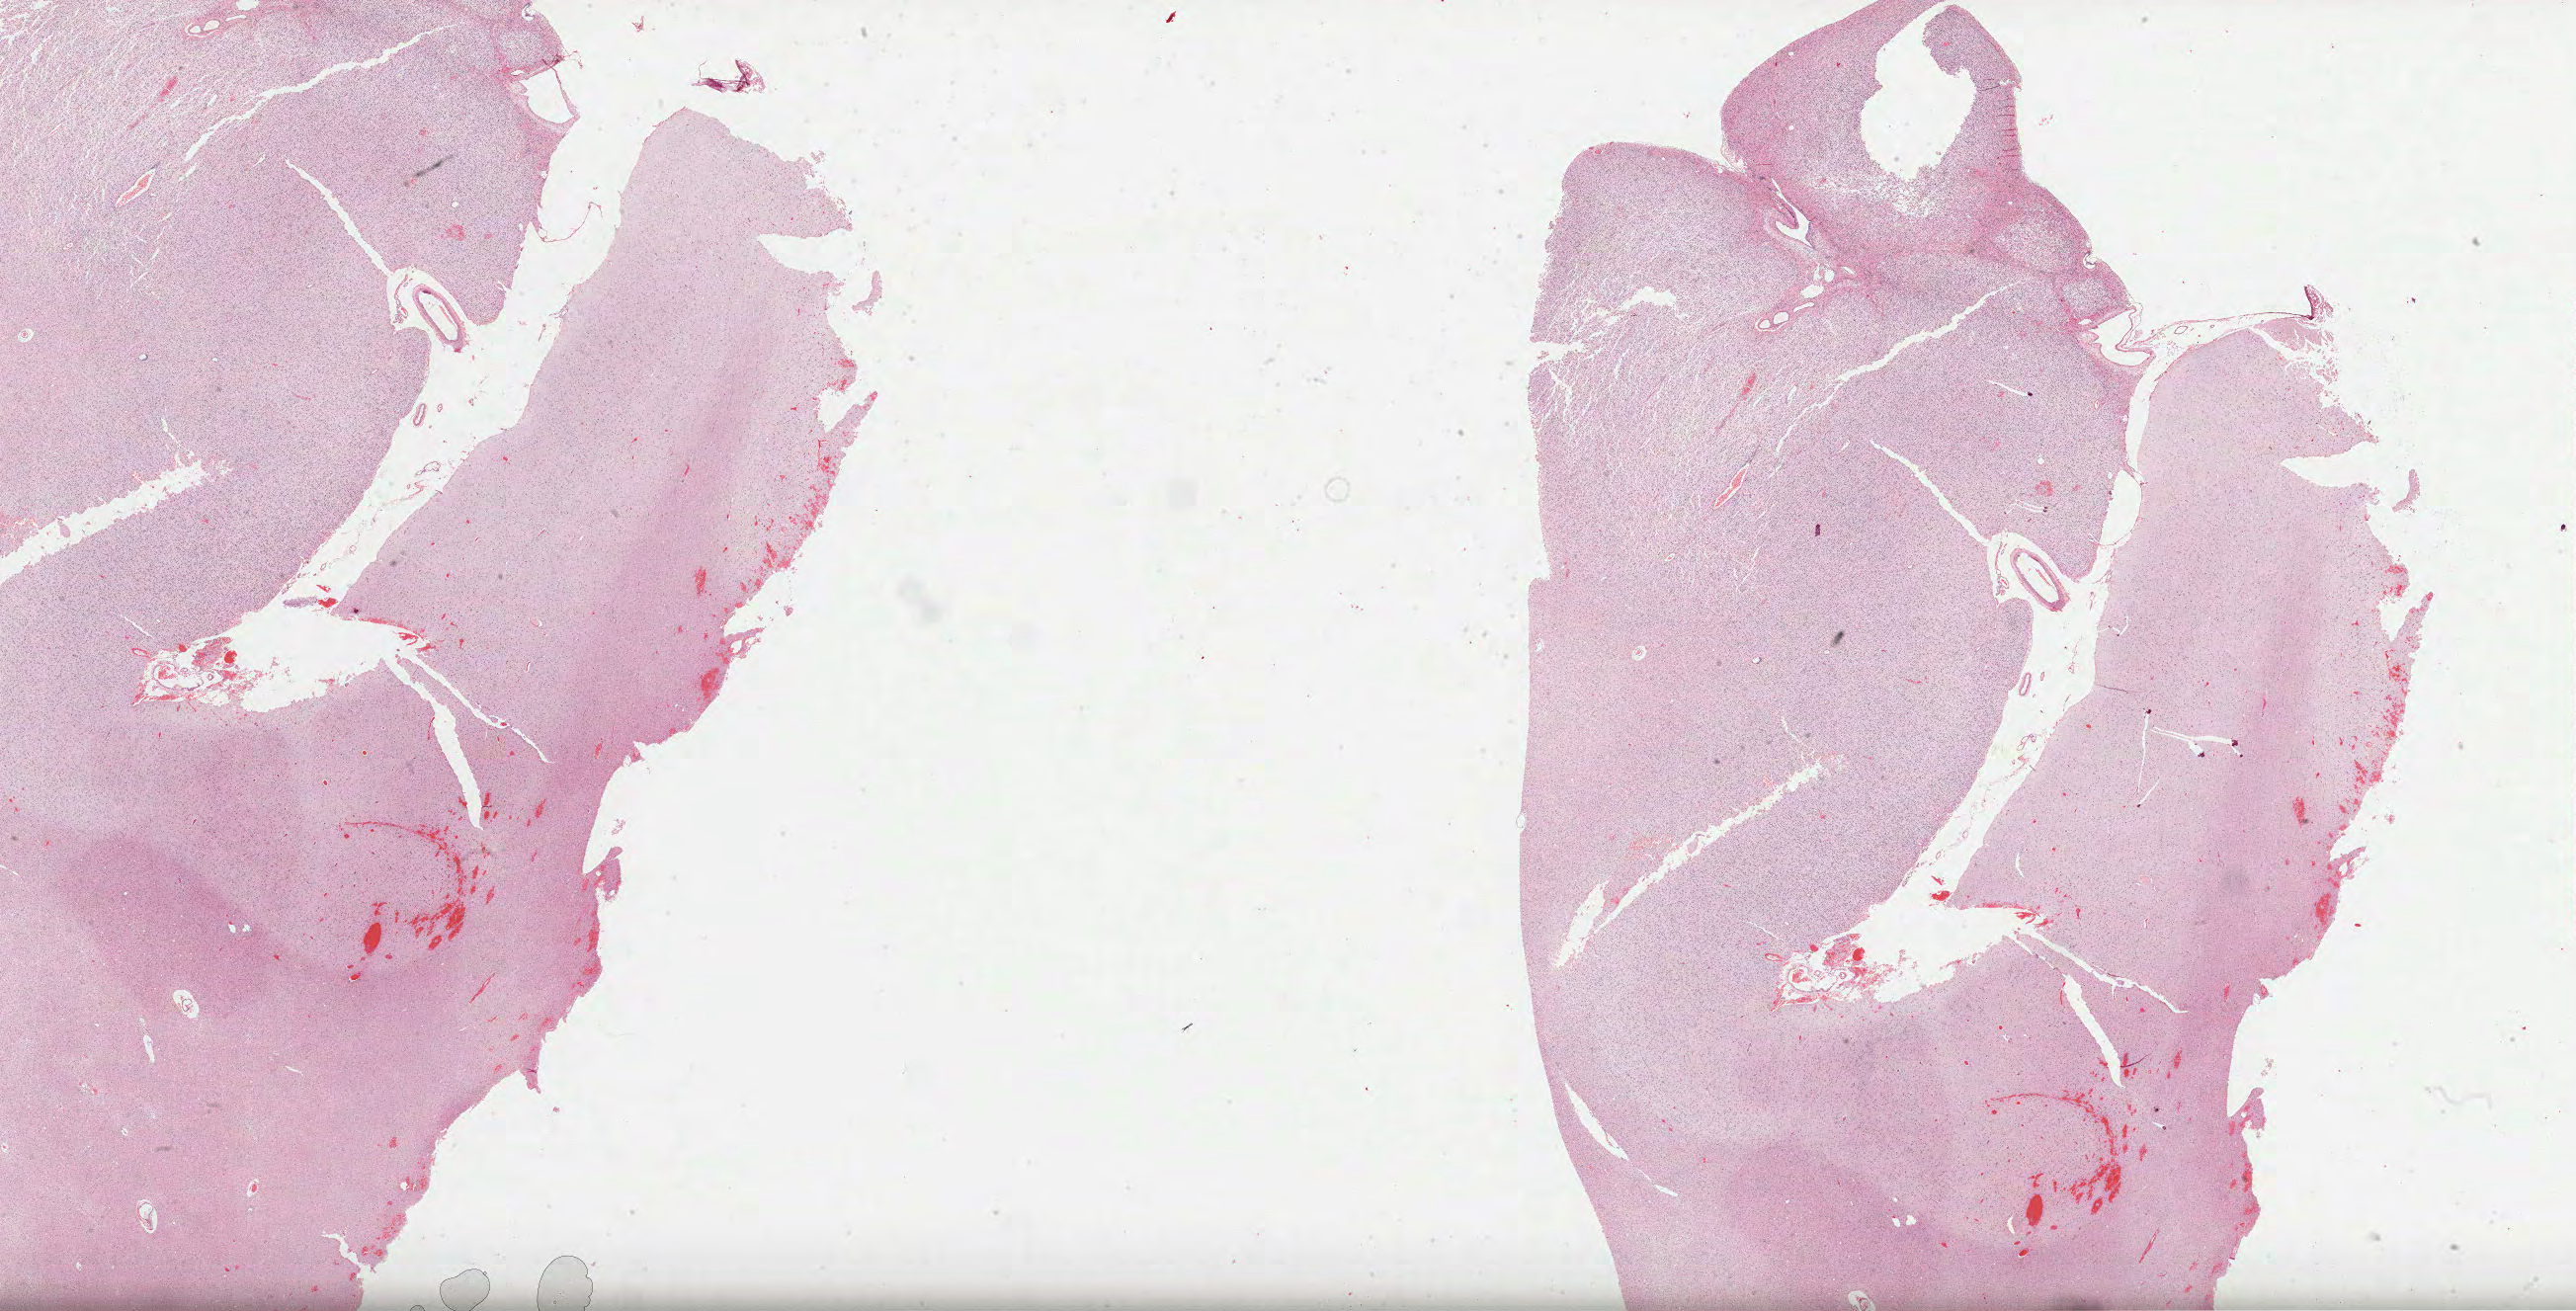
Whole-slide histology image, Hematoxylin and eosin (H&E) stained, shown as a low-resolution overview of the whole scanned area (about 42.1 x 21.4 mm). Formalin-fixed paraffin-embedded (FFPE) diagnostic section. Primary tumour sample from the brain. Female patient; age at initial diagnosis 39 years. Histologic grade: G2 (moderately differentiated).
Pathologic diagnosis: Mixed glioma (cerebrum).